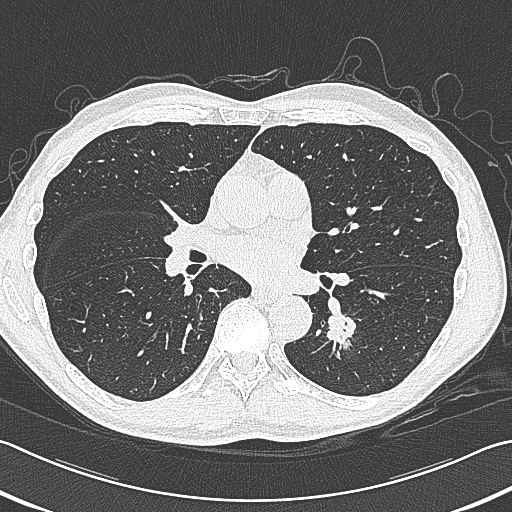
Low-dose screening chest CT, axial slice. Baseline screening round. Lung window (W 1500 / L -600 HU). 1 mm slice thickness. Slice 174 of 354 in the series. Male participant, aged 59 years at enrolment. Former smoker at enrolment.
- Lesion marked by an expert reader, bounding box <313,294,376,352> (left, top, right, bottom; pixels).
- The exam's reader record, not a measurement of the box and not confirmed to be the same lesion: non-calcified nodule or mass ≥4 mm, left lower lobe, 15 × 15 mm, smooth margins, soft tissue attenuation.
- Lung cancer was diagnosed 17 days after this screen: squamous cell carcinoma, large cell, nonkeratinizing, NOS, left lower lobe, poorly differentiated (G3), stage IB (AJCC 6th edition), 31 mm at pathology.